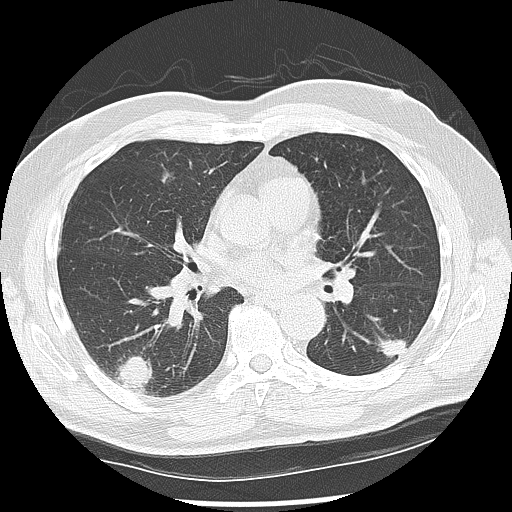
Low-dose screening chest CT, one axial slice. Reconstruction kernel LUNG. 120 kVp. Lung window (W 1500 / L -600 HU). 512 × 512 image matrix, field of view 360 × 360 mm.
Outlined on this slice (outlined manually by an expert reader):
- lesion 1 (nodule, lower lobe of left lung): bounding box <375,336,407,358> (left, top, right, bottom; pixels)
- lesion 2 (nodule, lower lobe of right lung): <116,356,153,390>